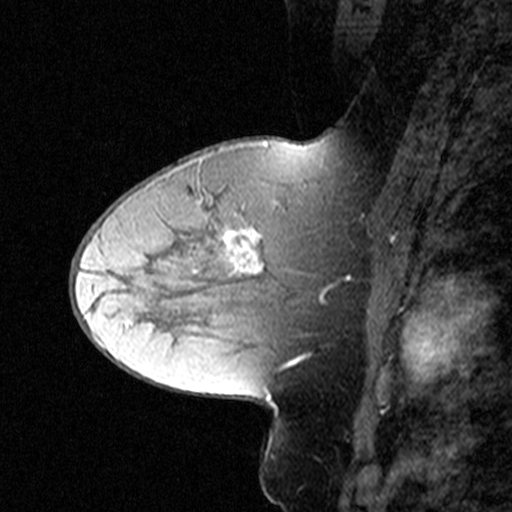
Breast MRI (dynamic contrast-enhanced), one sagittal slice. Slice 22 of 44 in the series (ordered by position). Dynamic contrast-enhanced study with each time point stored as its own series, time point 2 of 3 at this slice position (early post-contrast, ordered by acquisition time). 1.5 T. TE 4.5 ms, TR 11 ms. 3 mm slice thickness. 512 × 512 image matrix. Female patient, age 50 years. Case-level facts recorded for this patient, not image findings: setting: breast cancer imaged before/during neoadjuvant chemotherapy; receptor status: HR-positive, HER2-negative.
Outlined on this slice (semi-automatic segmentation, software-assisted and operator-edited):
- analysis volume of interest (the breast-tissue region the enhancement analysis was run in; not a lesion): bounding box (x1, y1, x2, y2) in pixels: (180, 198, 349, 311)
- tumour enhancement mask (voxels above the 90 % enhancement threshold inside the analysis volume of interest): (208, 213, 349, 304)